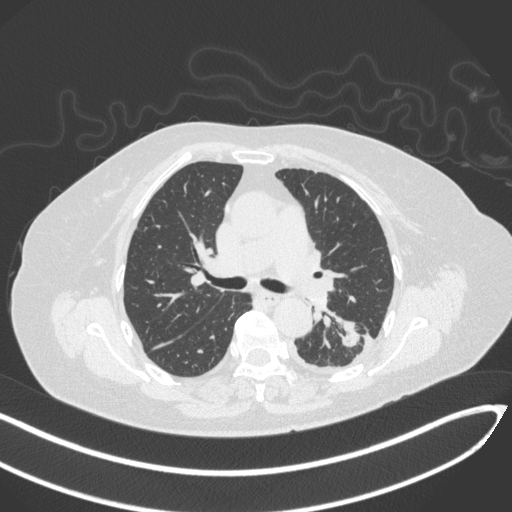
Chest CT, one axial slice; slice 195 of 270 in the series (ordered by position); lung window (W 1500 / L -600 HU); 1 mm slice thickness; 512 × 512 image matrix. Female patient, age 76 years. From the clinical record (not read from this slice): clinical TNM (as recorded): T1c N0 M0.
Outlined on this slice (rectangle marked by the reading radiologist):
- lung tumour (recorded histology: adenocarcinoma): bounding box <336,321,362,350> (left, top, right, bottom; pixels)